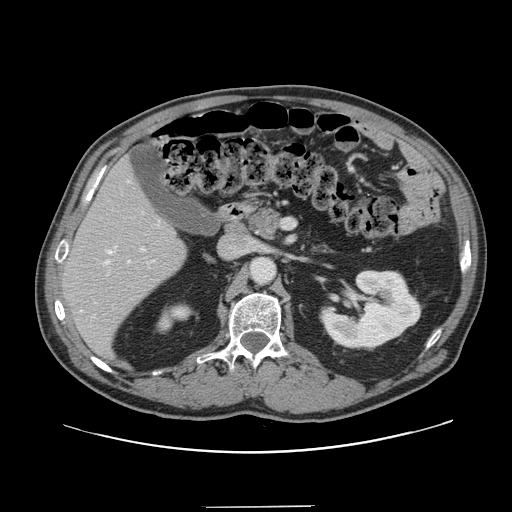
Contrast-enhanced abdominal CT, one axial slice. Slice 75 of 139 in the series (ordered by position). 120 kVp. Intravenous contrast given. Soft-tissue window (W 400 / L 40 HU). 512 × 512 image matrix. Male patient, age 64 years. Case-level facts recorded for this patient, not image findings: diagnosis: colorectal cancer liver metastases, imaged before liver resection; multiple liver metastases: yes; largest metastasis: 3.5 cm.
Annotated regions visible in this slice (outlined manually by an expert reader):
- hepatic veins: bounding box [x1, y1, x2, y2] px = [105, 180, 159, 264]
- liver: [64, 162, 185, 355]
- planned liver remnant (the part of the liver to remain after resection): [63, 162, 186, 356]
- portal vein (with intrahepatic branches): [107, 247, 145, 275]